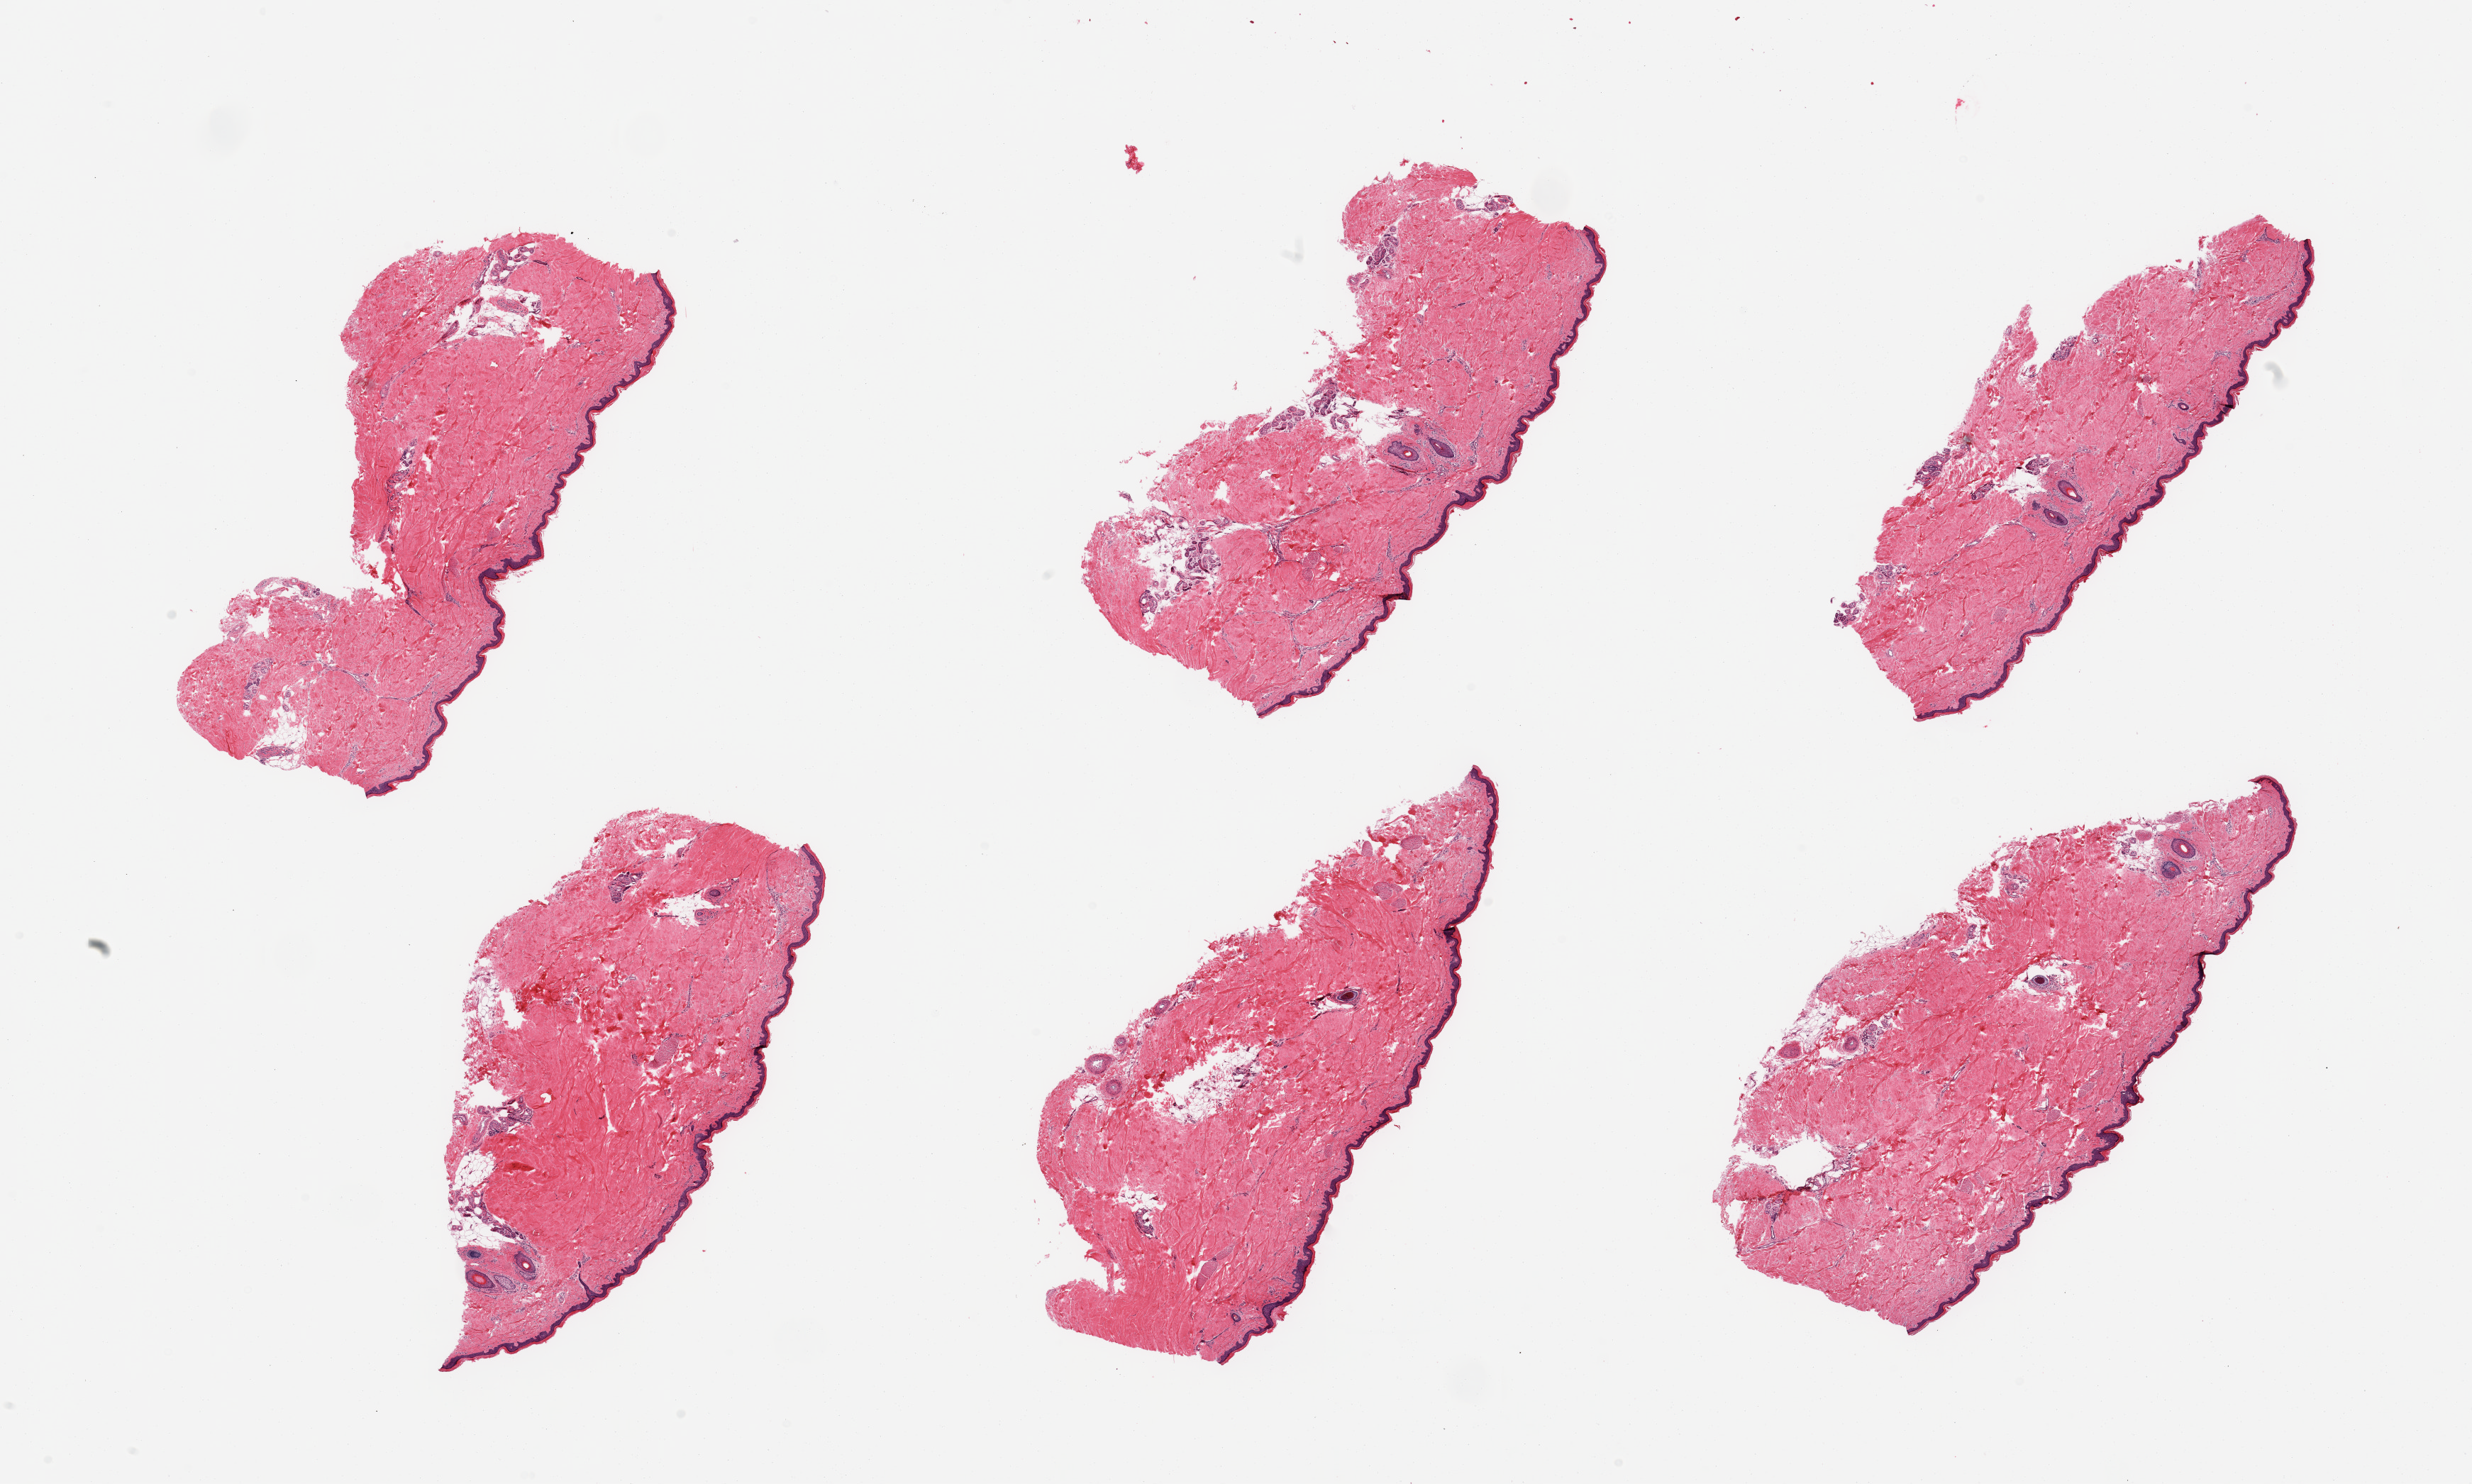
Whole-slide image, H&E stain, a low-resolution overview of the entire scanned area, about 27.6 x 16.5 mm; PAXgene-fixed paraffin-embedded (PFPE) section; sampled site (target tissue): skin of lower leg; donor tissue sample.
Review note (as recorded): 6 pieces; well trimmed; 5% dermal fat.